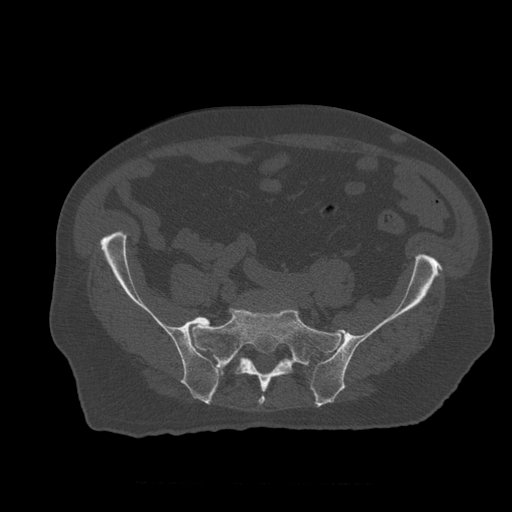
CT including the spine, one axial slice. Slice 120 of 399 in the series (ordered by position). Bone window (W 1800 / L 400 HU). 1.25 mm slice thickness. 512 × 512 image matrix, field of view 407 × 407 mm. Patient age 73 years. From the clinical record (not read from this slice): primary cancer: prostate; vertebrae with lytic lesions (as recorded): L2.
Structures marked on this image (semi-automatically segmented with operator editing):
- L5 vertebra: bounding box <213,361,226,376> (left, top, right, bottom; pixels)